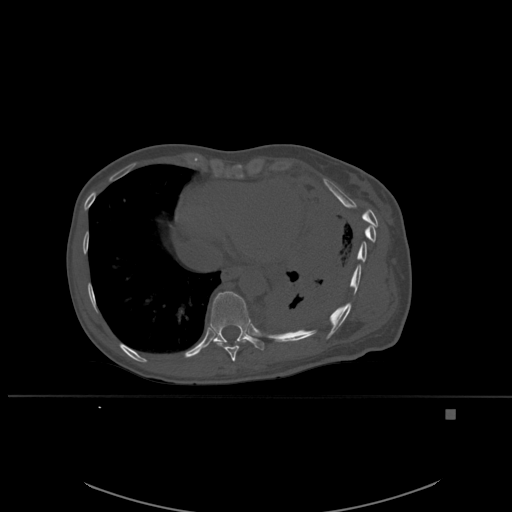
CT including the spine, one axial slice; slice 325 of 537 in the series (ordered by position); bone window (W 1800 / L 400 HU); 1.5 mm slice thickness; 512 × 512 image matrix. Patient: female, 45 years. Case-level facts recorded for this patient, not image findings: primary cancer: lung.
Structures marked on this image (semi-automatic segmentation, software-assisted and operator-edited):
- T10 vertebra: bounding box [x1, y1, x2, y2] px = [203, 291, 265, 350]
- T9 vertebra: [214, 339, 247, 362]